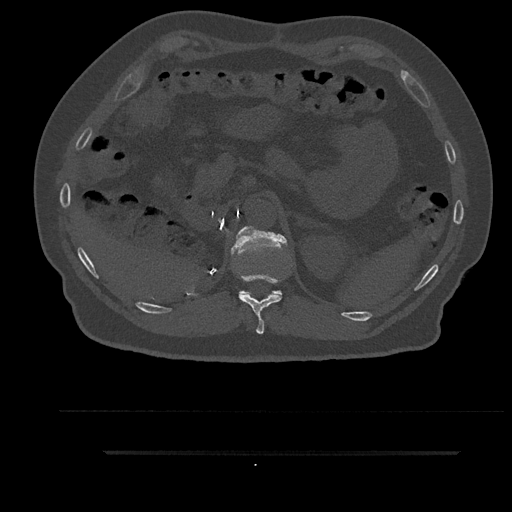
CT including the spine, one axial slice; slice 279 of 797 in the series (ordered by position); reconstruction kernel Br40s/3; 120 kVp; bone window (W 1800 / L 400 HU); 0.5 mm slice thickness; 512 × 512 image matrix, field of view 432 × 432 mm. Patient: male, 63 years. Case-level facts recorded for this patient, not image findings: primary cancer: renal; vertebrae with lytic lesions (as recorded): T8.
Structures marked on this image (semi-automatic segmentation, software-assisted and operator-edited):
- T11 vertebra: bounding box <239,234,282,334> (left, top, right, bottom; pixels)
- T12 vertebra: <231,226,287,295>